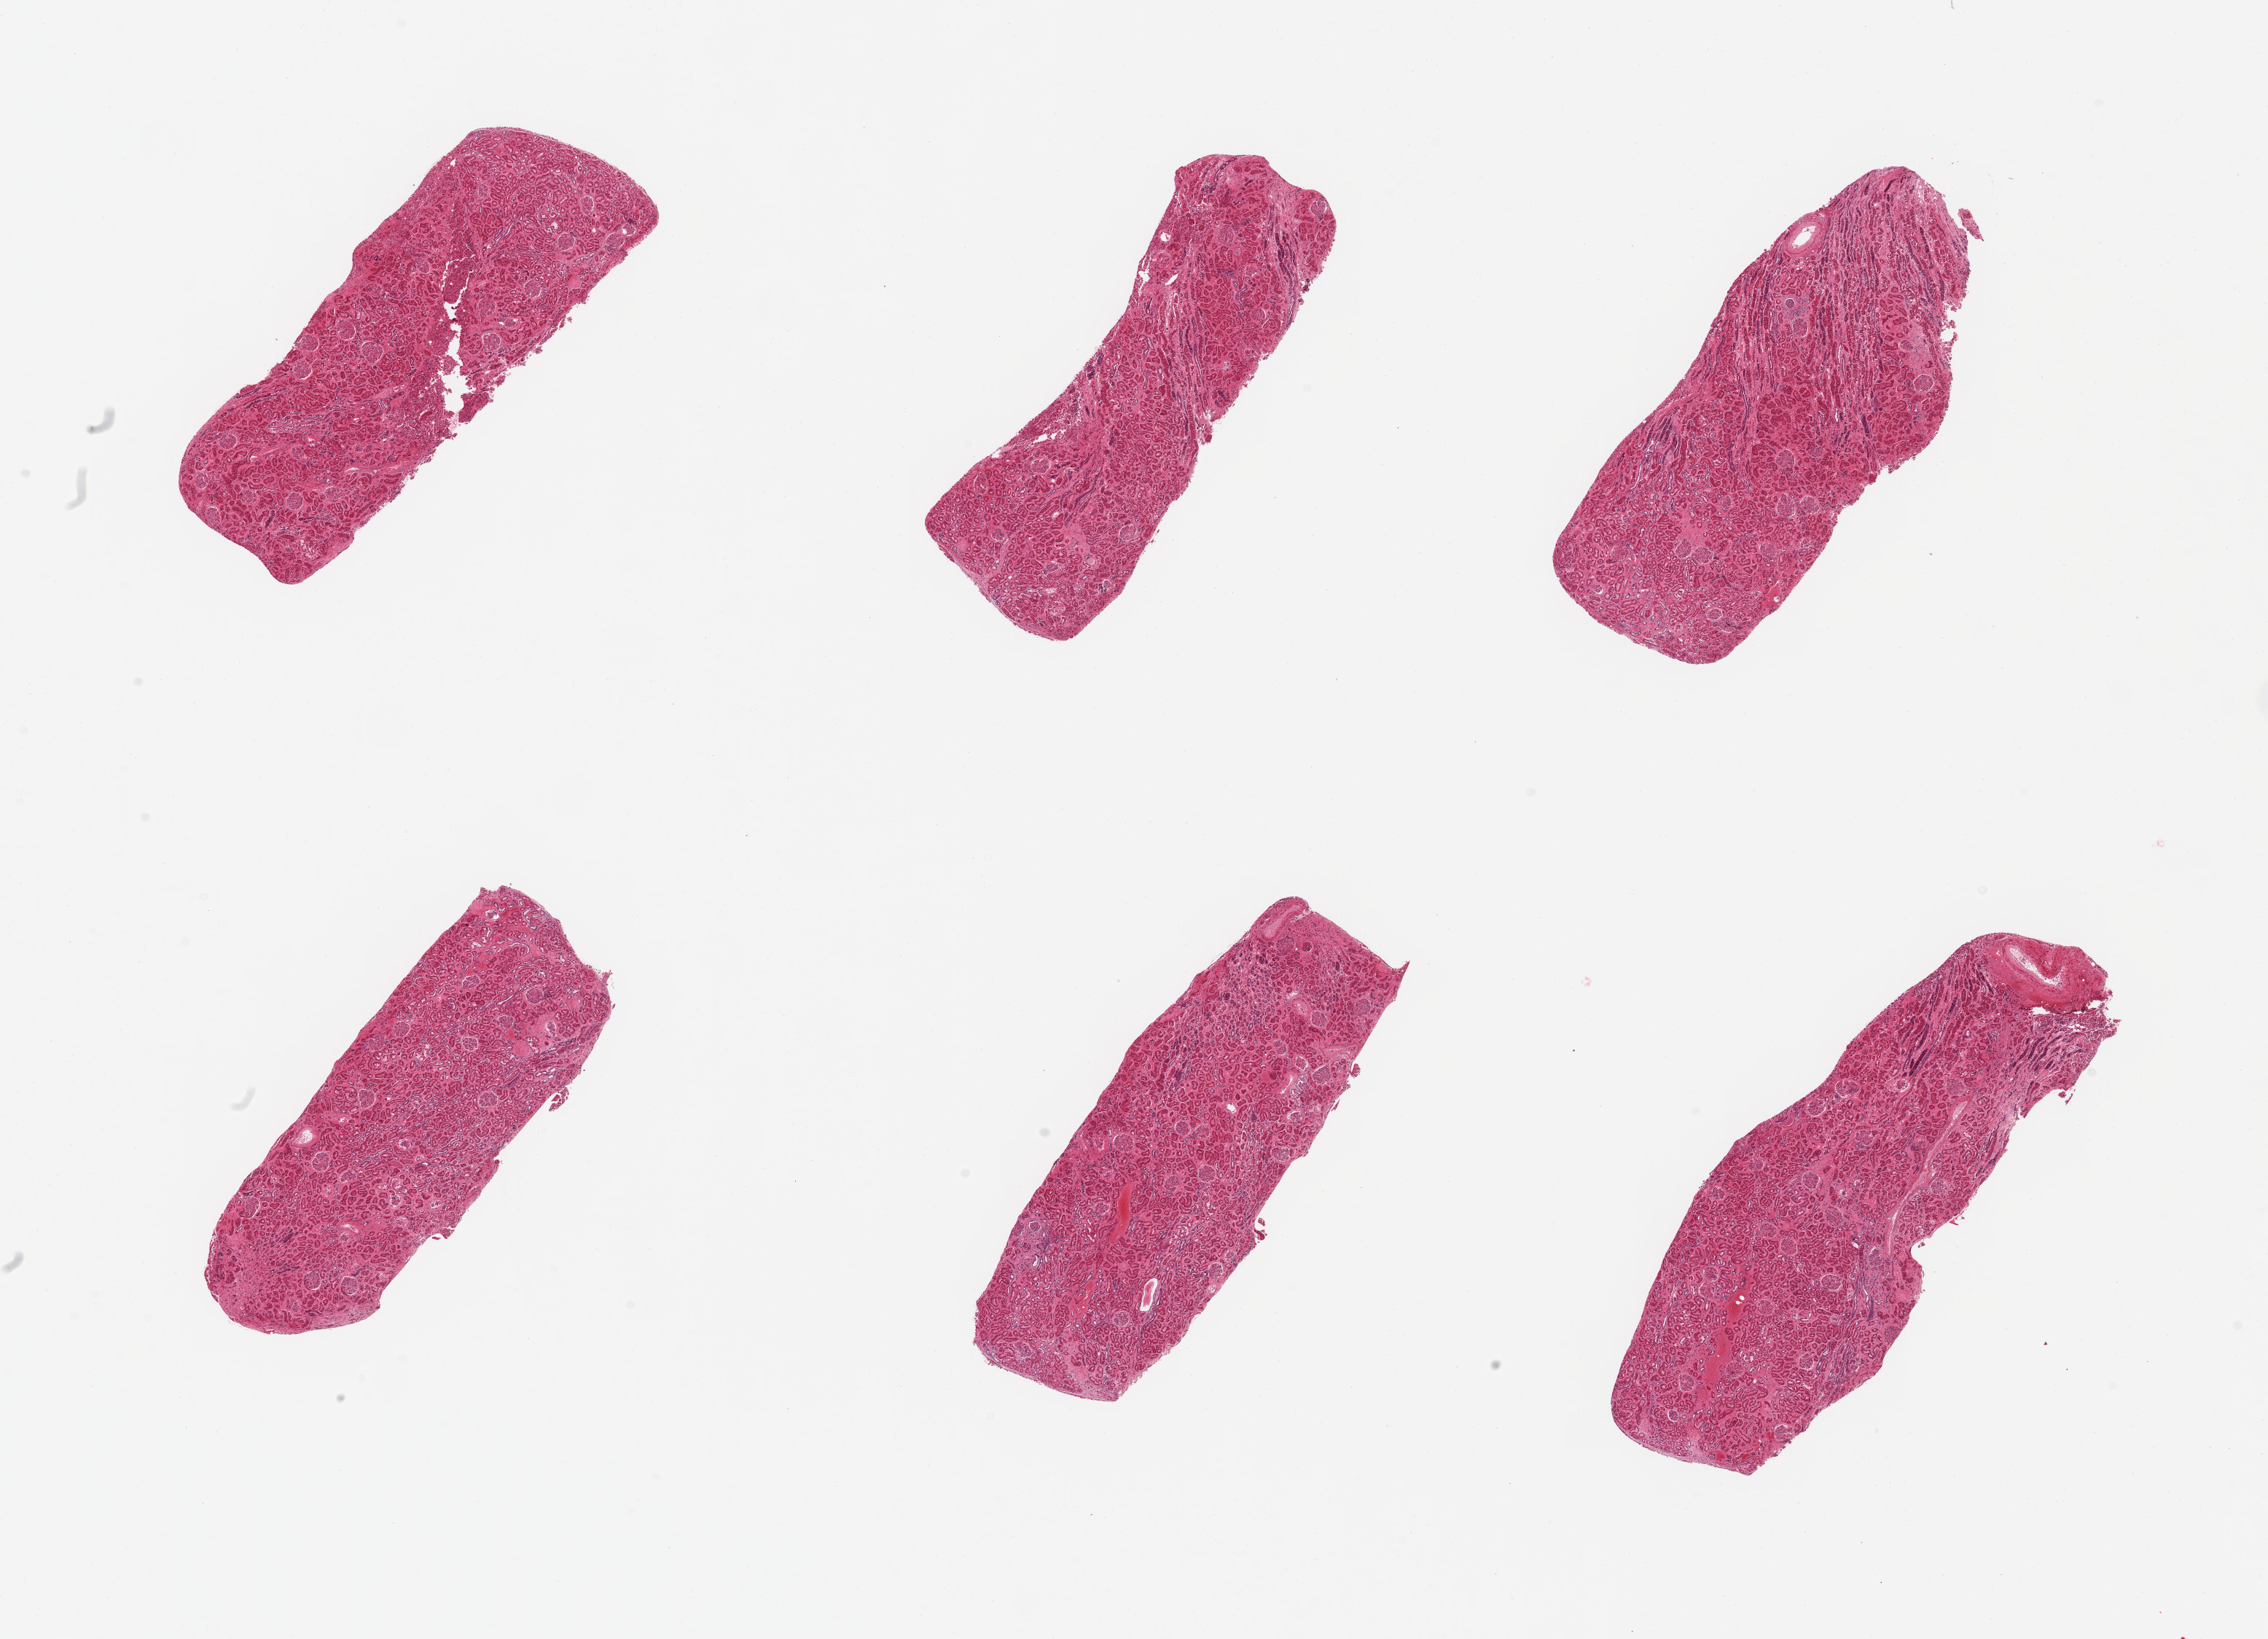
Hematoxylin and eosin (H&E) whole-slide image — low-resolution overview of the scanned area, about 24.6 x 17.8 mm, PAXgene-fixed paraffin-embedded (PFPE) section, target tissue: renal cortex, tissue donor sample. Female donor.
Review note (as recorded): 6 pieces; no chronic or acute lesions.